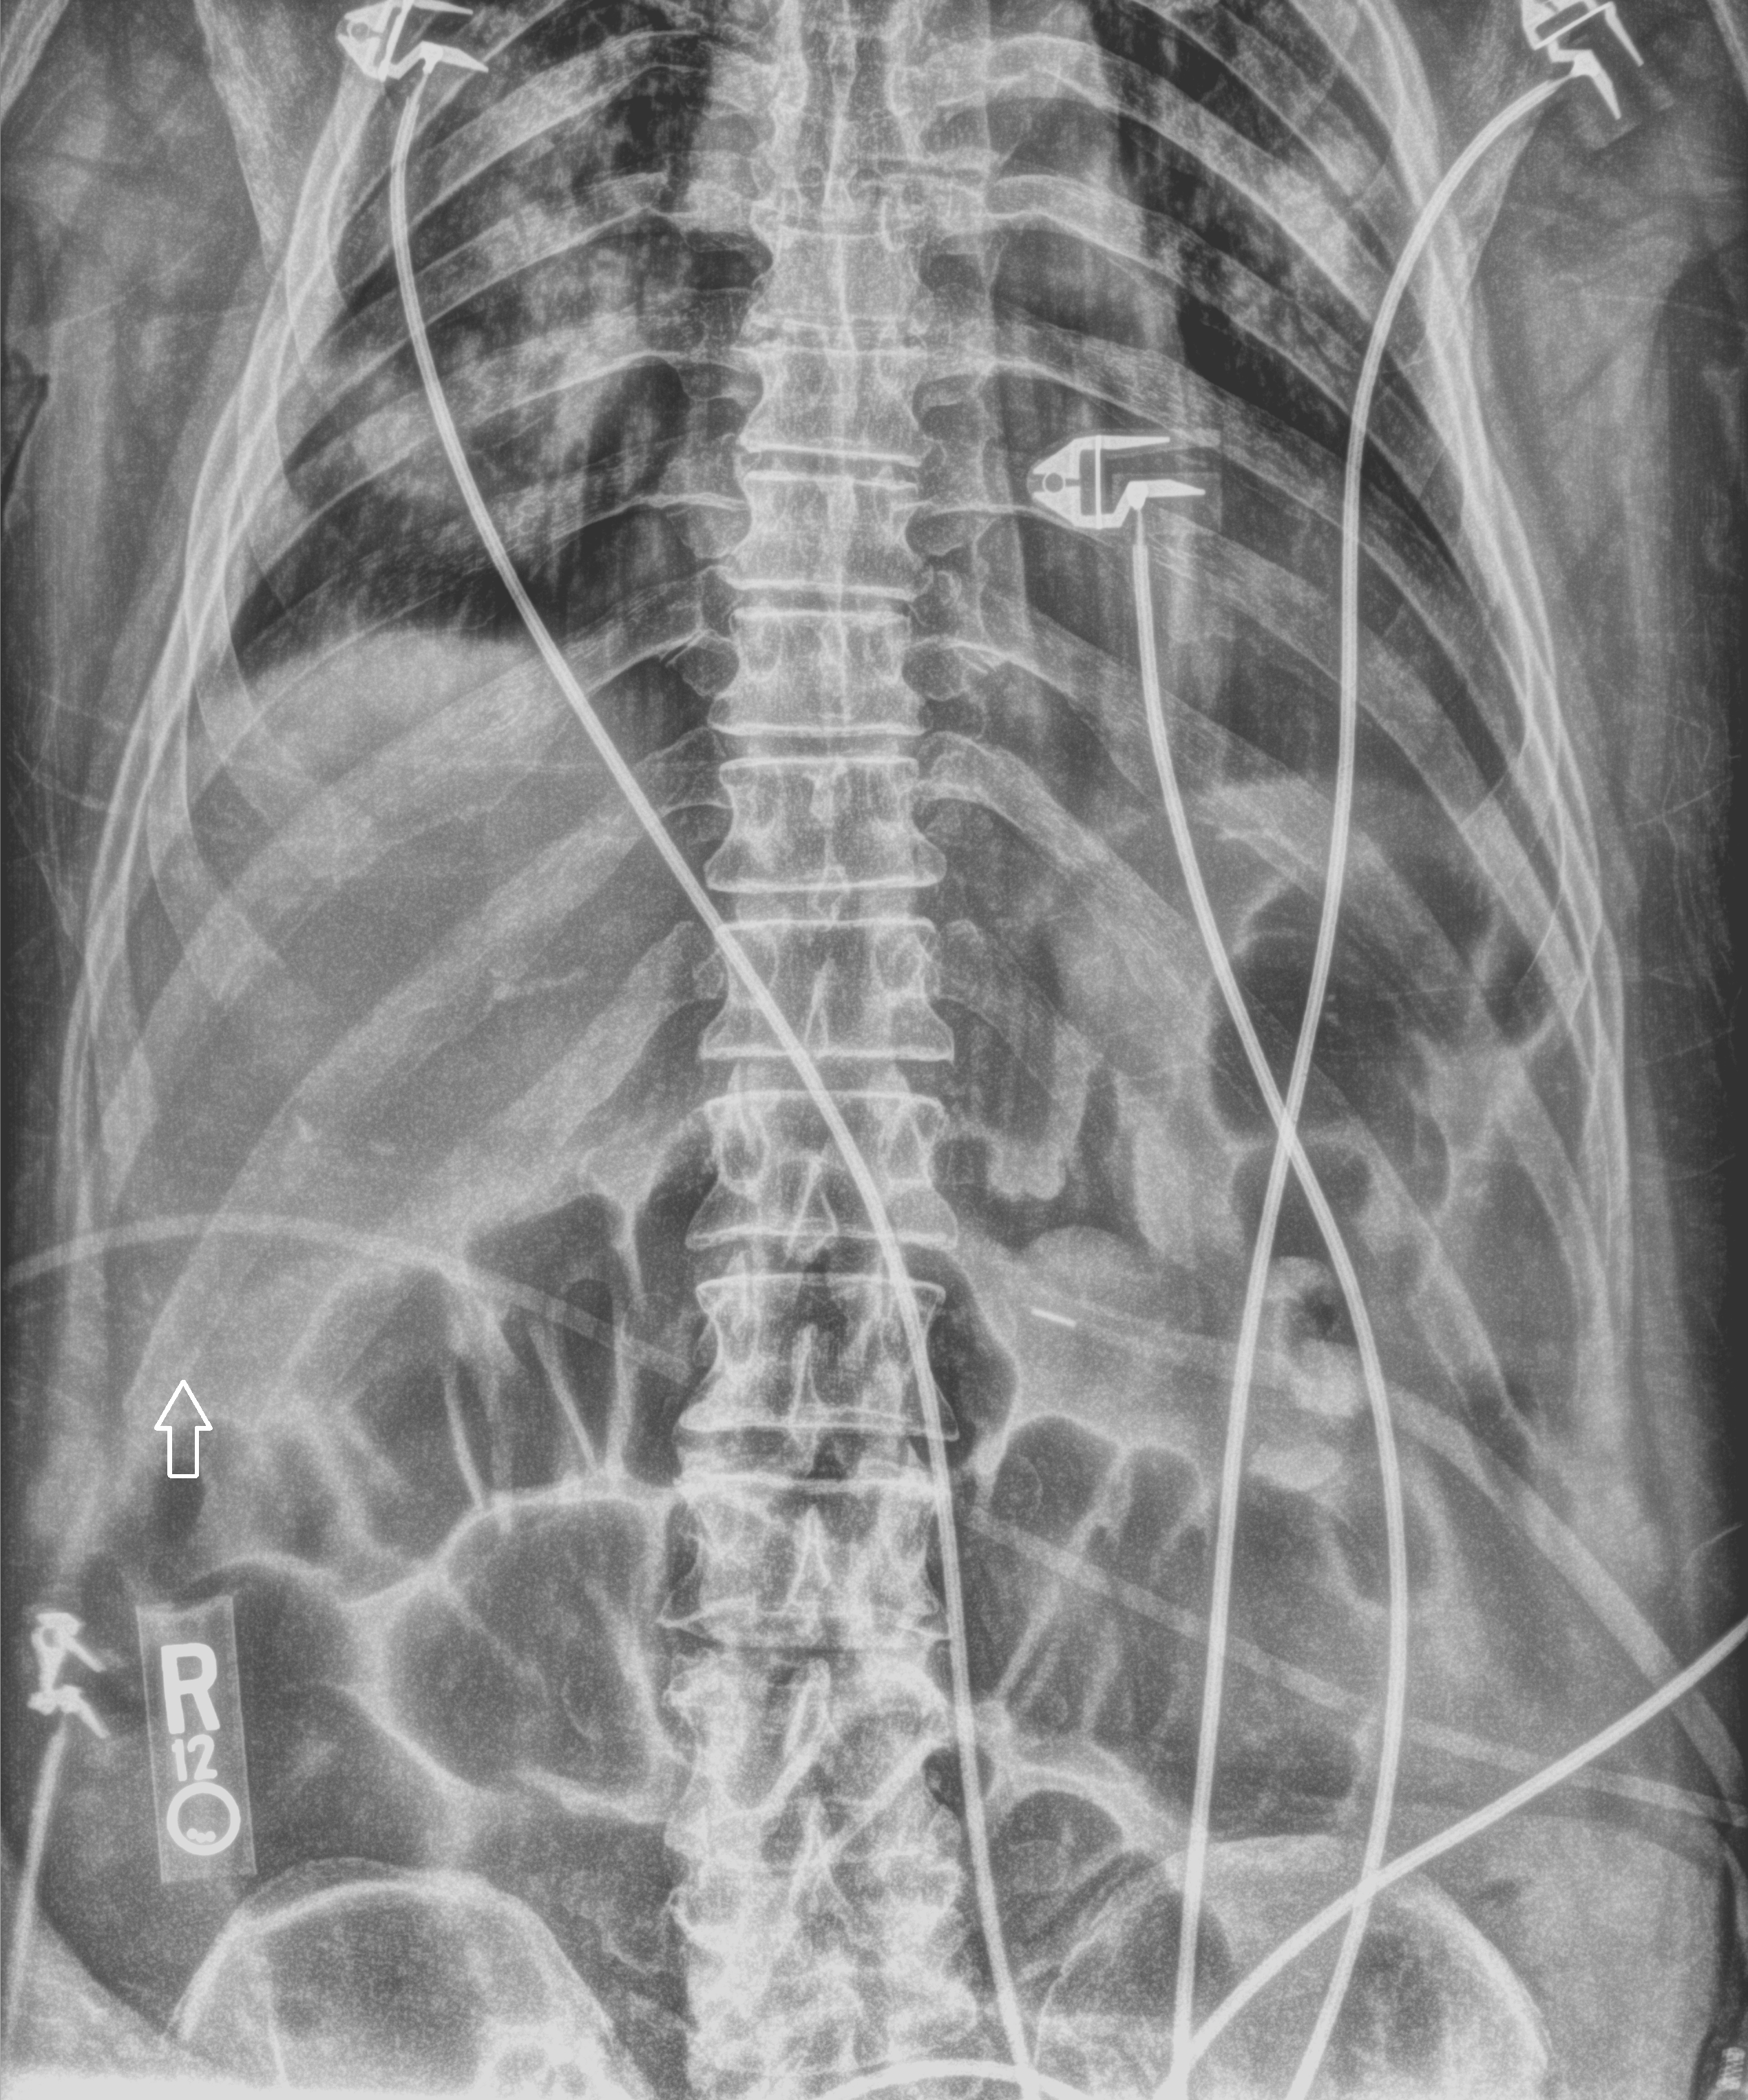
Portable abdomen radiograph, anteroposterior (AP) projection. Male patient hospitalised with COVID-19, age 60–74 years.
Hospital-stay facts (about this admission, not read from this image; timing relative to this image not recorded): chronic kidney disease (admission record): no; mechanically ventilated during this hospital stay: no; admitted to intensive care during this hospital stay: no.